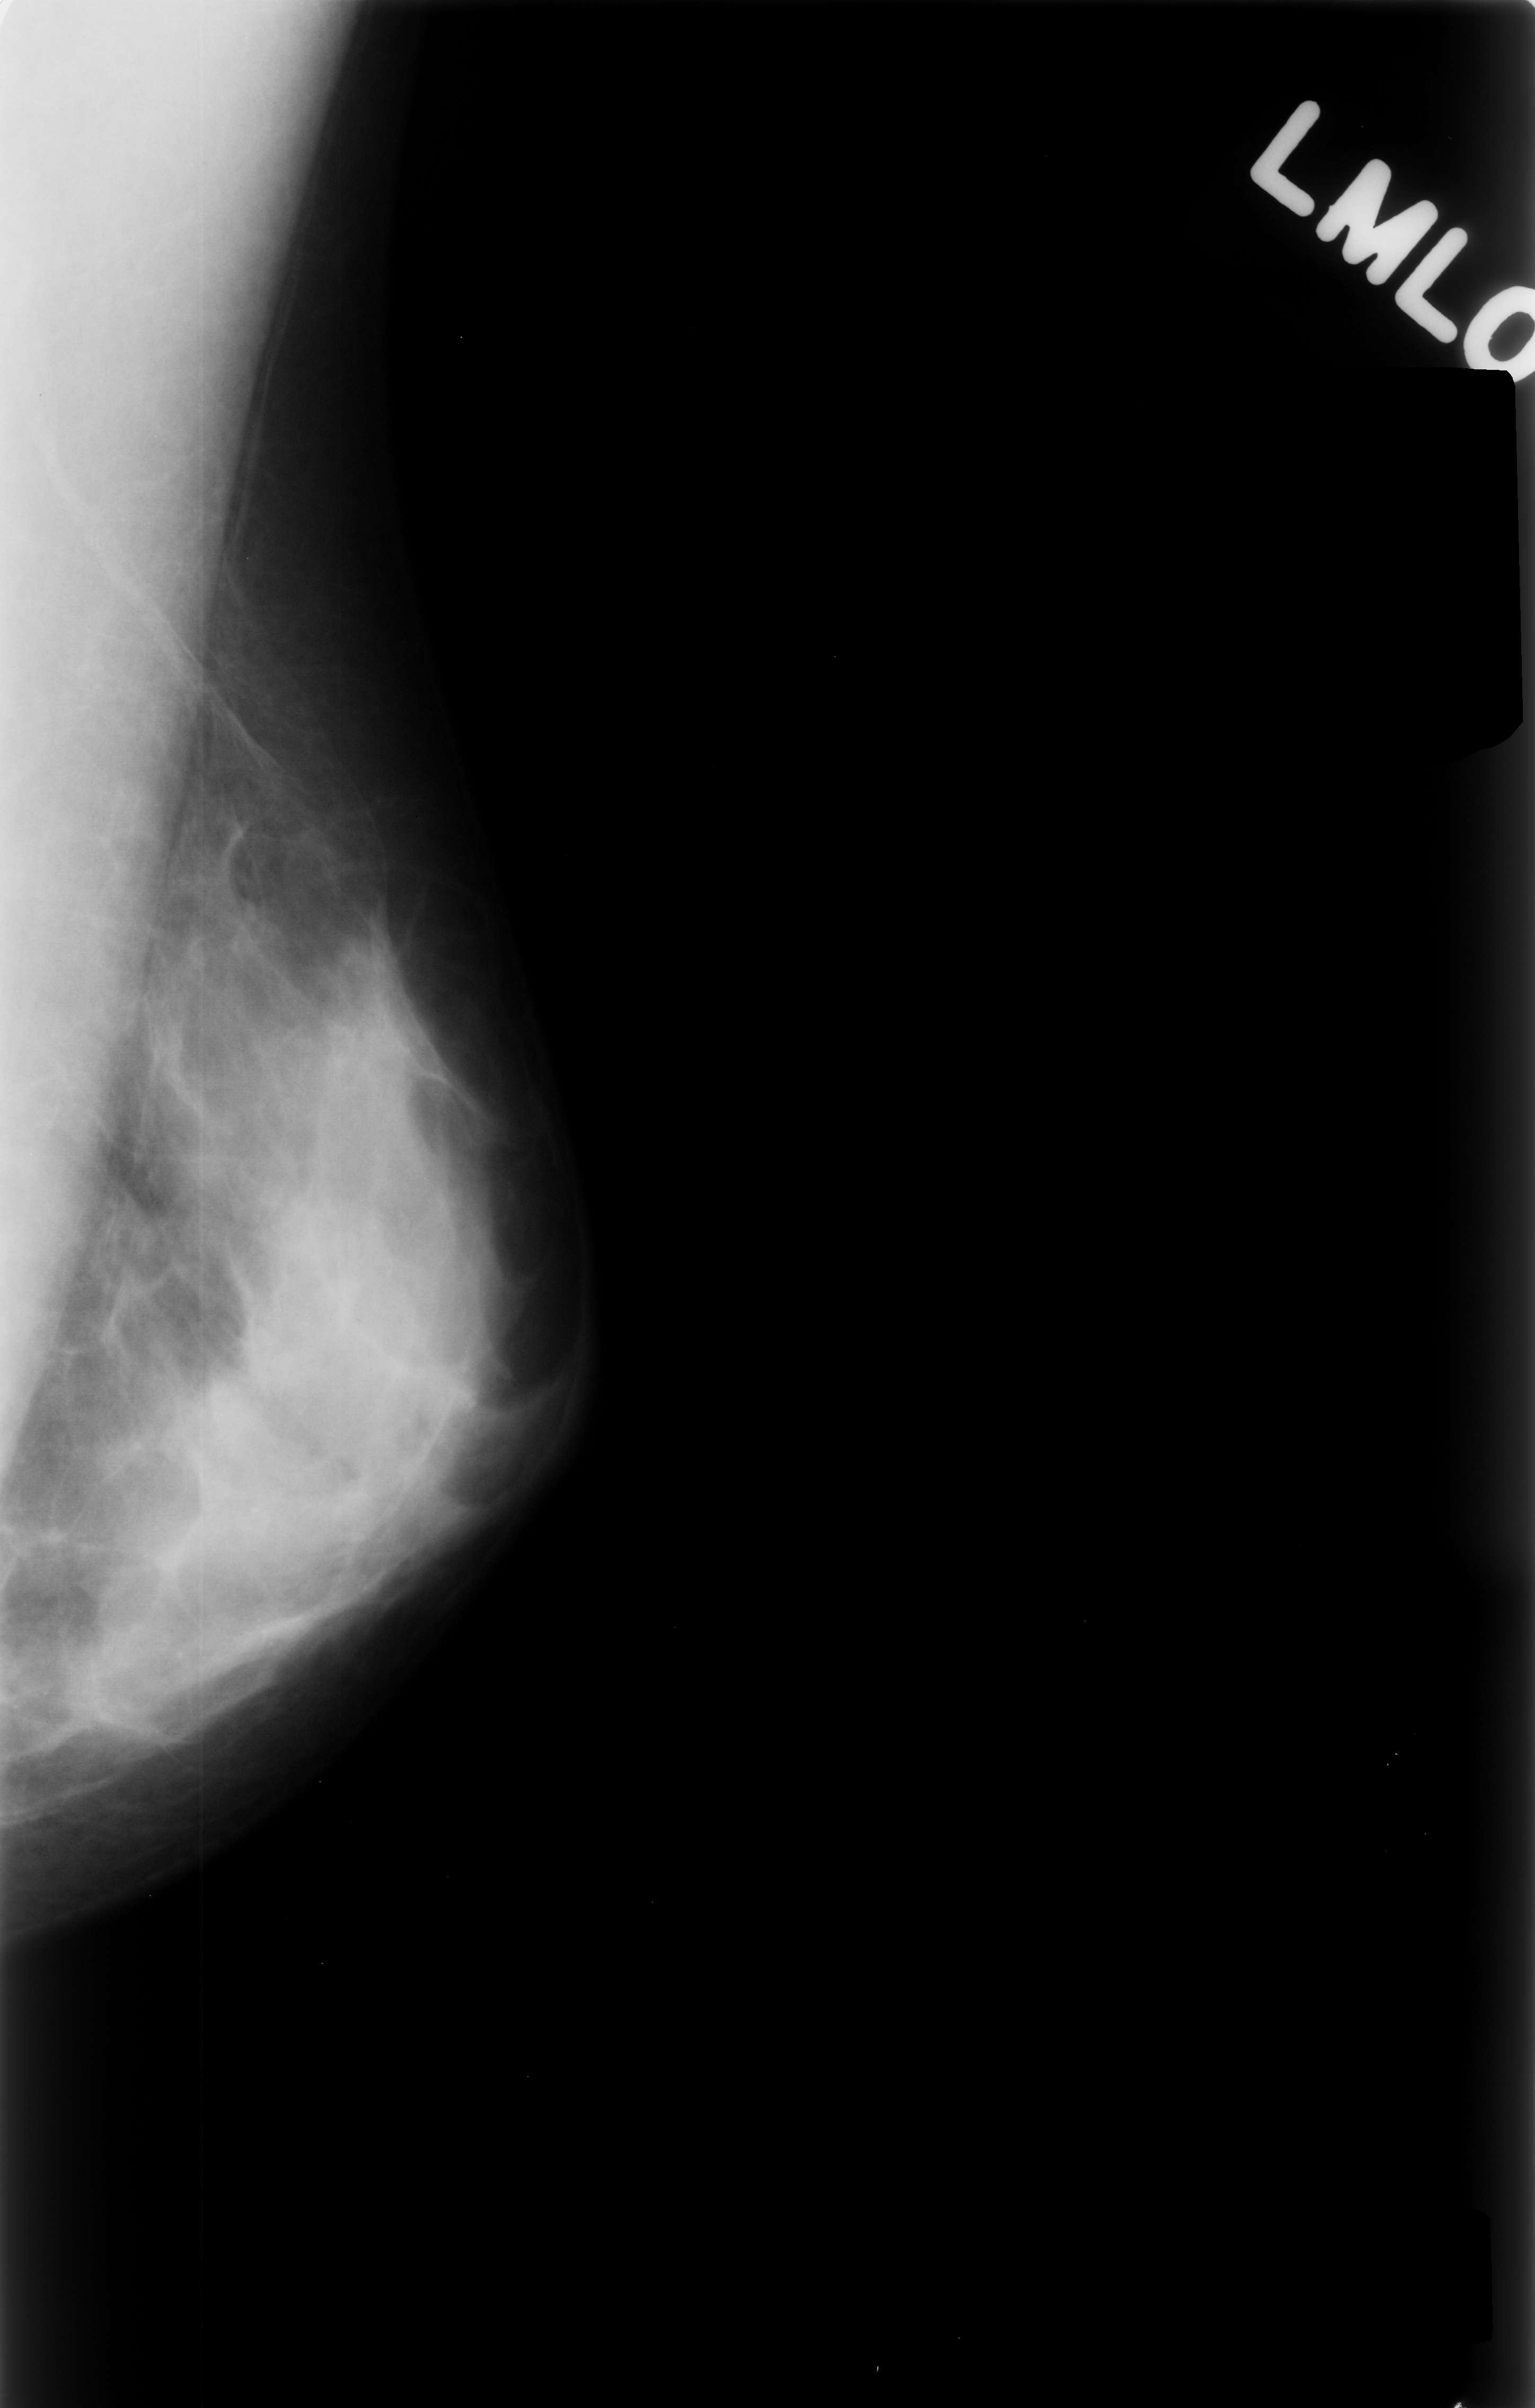
Mammogram (digitized film). Left breast. Mediolateral oblique (MLO) view. 1535 × 2408 image matrix.
Expert-marked regions of interest on this film, with their recorded descriptors:
- calcifications, morphology punctate, distribution clustered; BI-RADS assessment category 4; pathology (as recorded): benign: bounding box (x1, y1, x2, y2) in pixels: (195, 1551, 357, 1731)